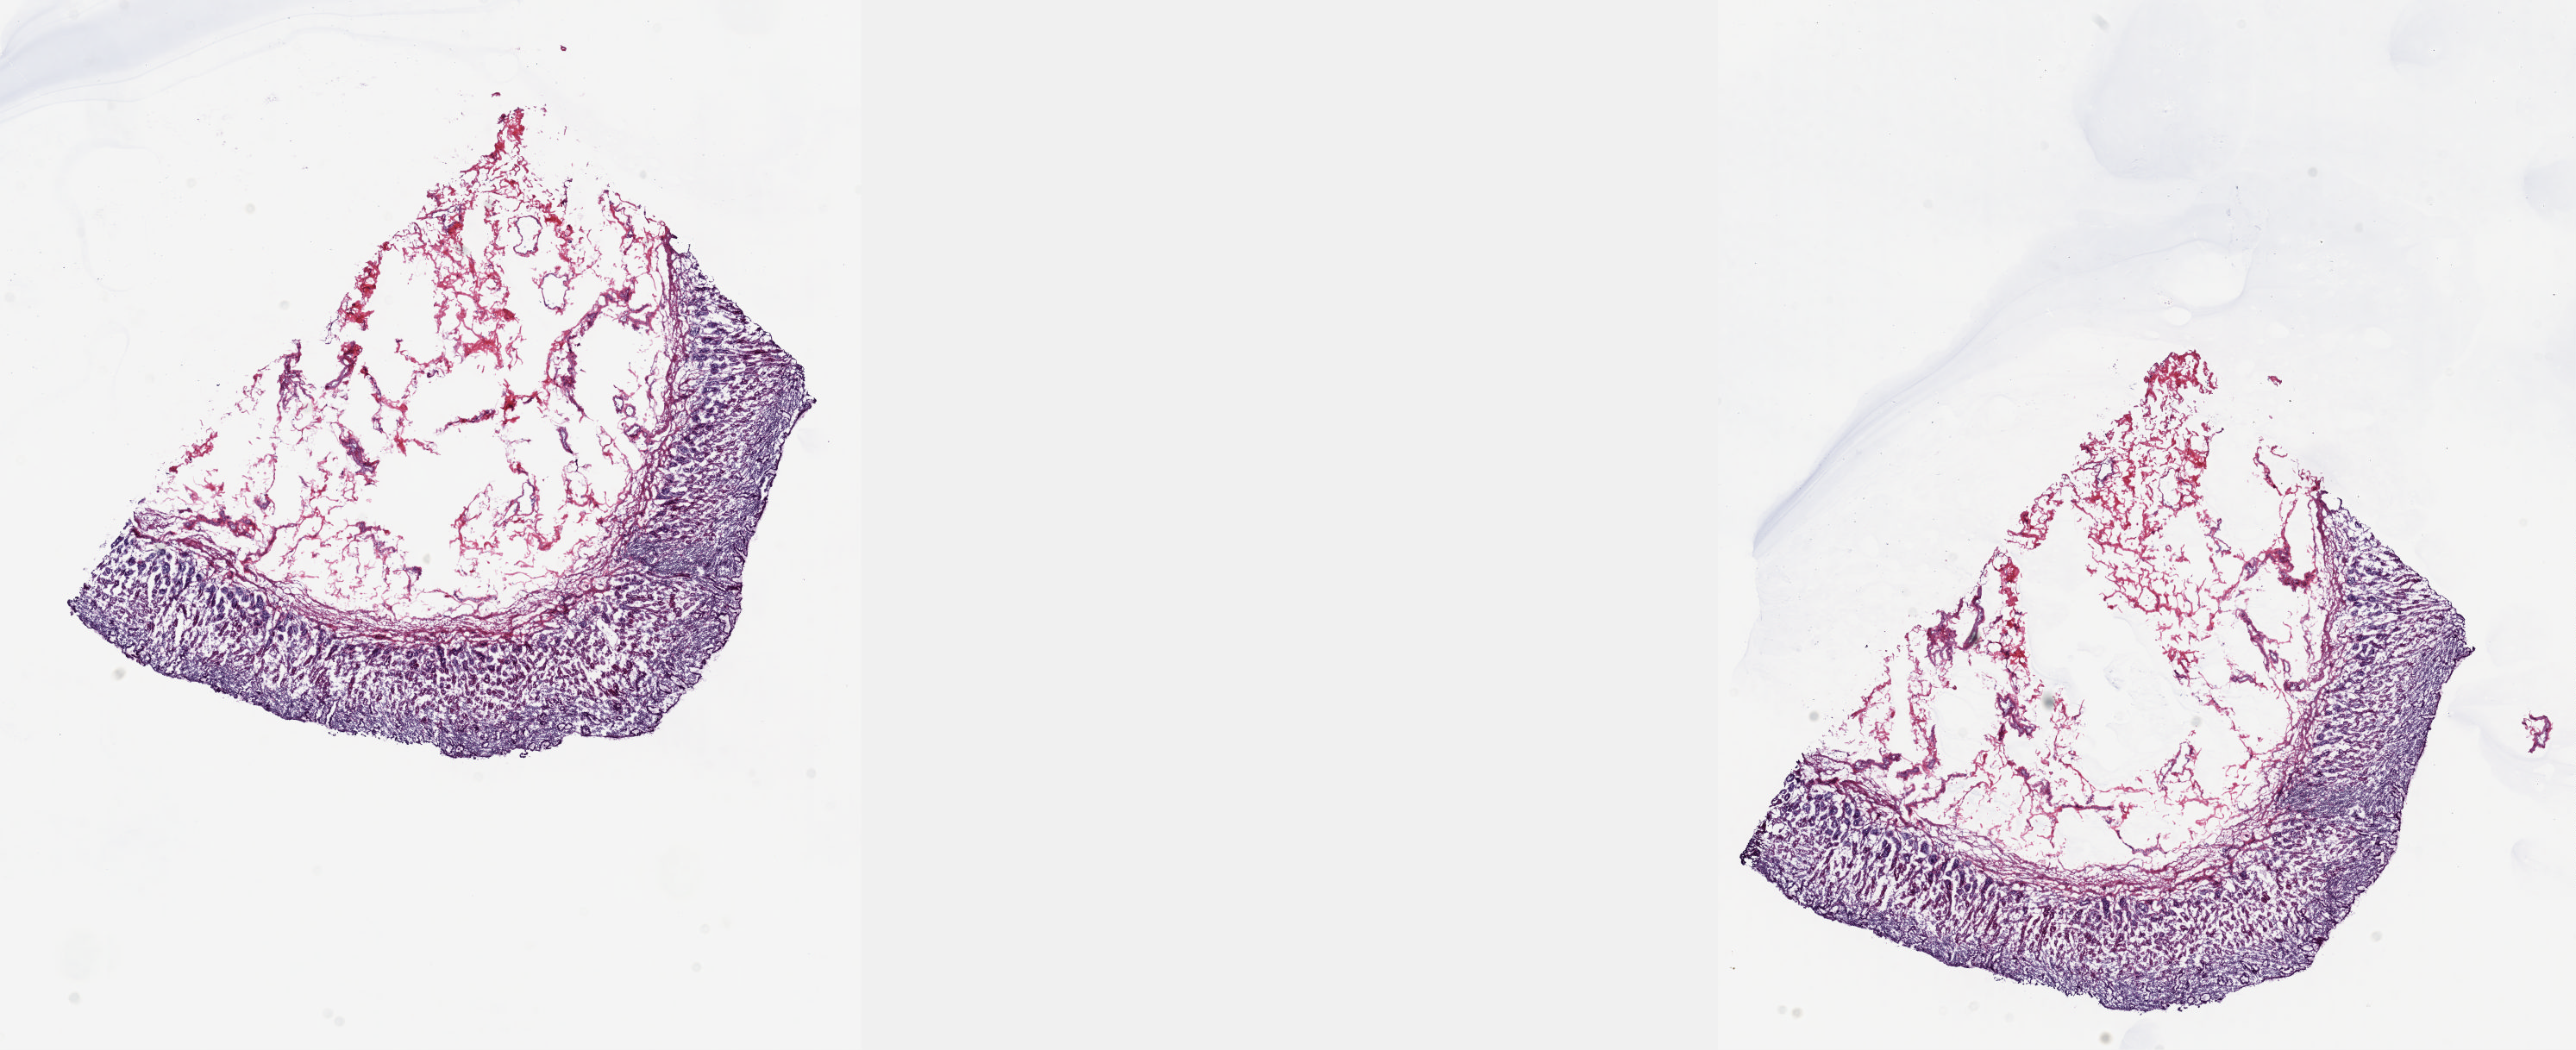
Whole-slide histology image, H&E-stained, a low-resolution overview of the entire scanned area, about 24.1 x 9.8 mm (from a 20x scan), frozen section from the top of the tissue portion, solid tissue normal (non-tumour tissue) sample from the pancreas. Female patient; age at initial diagnosis 80 years. Composition of this section per pathologist review: tumour cells 0%, tumour nuclei 0%, normal cells 100%, stromal cells 0%, necrosis 0%. Inflammatory infiltration, as recorded: lymphocyte infiltration 3%, monocyte infiltration 0%, neutrophil infiltration 0%.
This section: solid tissue normal (non-tumour) sample from the same patient. Patient diagnosis: Infiltrating duct carcinoma, NOS (head of pancreas).